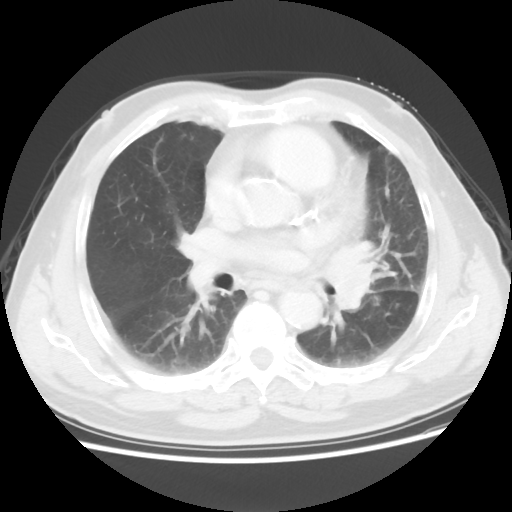
Chest CT, one axial slice; slice 31 of 56 in the series (ordered by position); reconstruction kernel STANDARD; 120 kVp; lung window (W 1500 / L -600 HU); 5 mm slice thickness; 512 × 512 image matrix, field of view 360 × 360 mm. Patient: male, 75 years. Case-level facts recorded for this patient, not image findings: clinical TNM (as recorded): T3 N0 M0.
Structures marked on this image (bounding box drawn by a radiologist):
- lung tumour (recorded histology: squamous cell carcinoma): bounding box (x1, y1, x2, y2) in pixels: (321, 232, 385, 314)